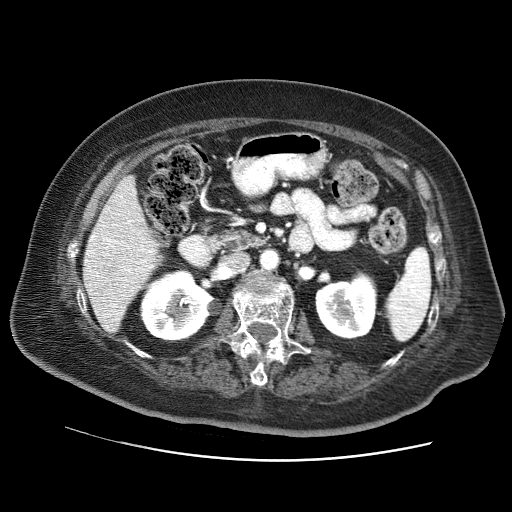
Contrast-enhanced abdominal CT (liver protocol), one axial slice. Slice 27 of 73 in the series (ordered by position). Soft-tissue window (W 400 / L 40 HU). 2.5 mm slice thickness. 512 × 512 image matrix. Case-level facts recorded for this patient, not image findings: diagnosis: hepatocellular carcinoma (patient treated with transarterial chemoembolisation; whether this scan precedes or follows treatment is not stated here); TNM stage (as recorded): Stage-I; Child-Pugh class: A; tumour differentiation: well differentiated; tumour nodularity: uninodular.
Annotated regions visible in this slice (semi-automatic segmentation, software-assisted and operator-edited):
- liver parenchyma outside the tumour (the mass and vessels are separate outlines, so this box may not span the whole liver): bounding box (x1, y1, x2, y2) in pixels: (84, 176, 158, 330)
- liver vessels: (86, 195, 154, 316)